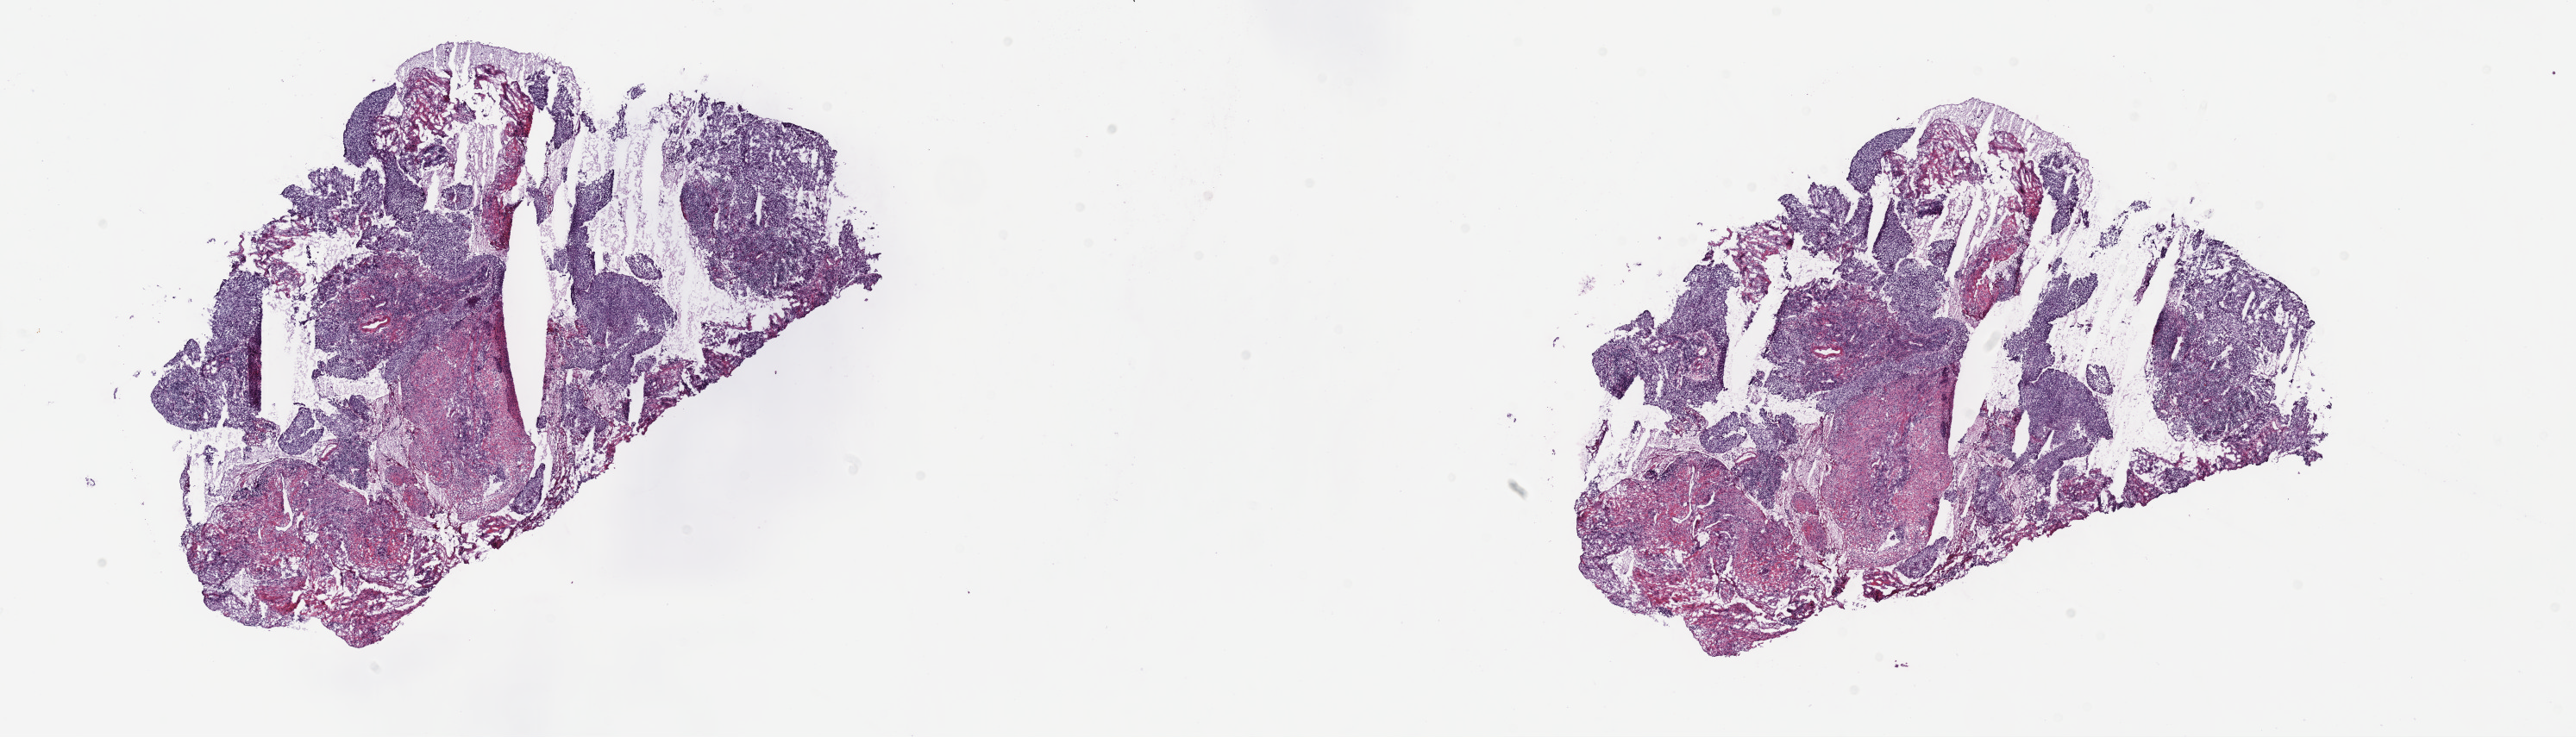
Whole-slide histology image, H&E-stained — whole scanned area (about 24.2 x 6.9 mm, from a 40x scan) shown as a low-resolution overview, frozen section from the top of the tissue portion, cervix, primary tumour sample. Patient: female, age at initial diagnosis 65 years. Histologic grade: G2 (moderately differentiated). Pathologist review of this section (percent, as recorded): tumour cells 60%, tumour nuclei 60%, normal cells 0%, stromal cells 30%, necrosis 10%. Infiltration values recorded for this section: lymphocyte infiltration 40%, monocyte infiltration 20%, neutrophil infiltration 20%.
FIGO stage: IVA. Pathologic diagnosis: Squamous cell carcinoma, NOS (cervix uteri).